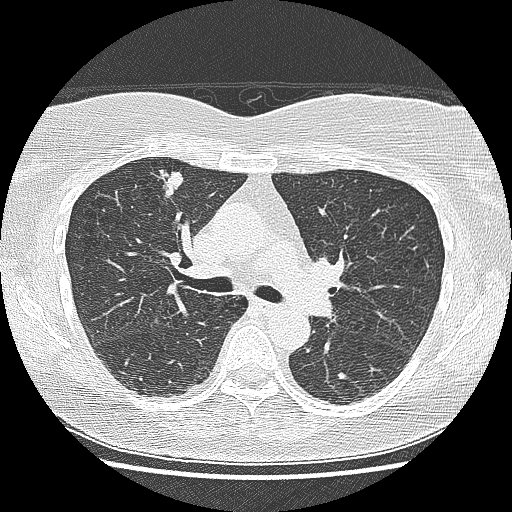
Low-dose screening chest CT, one axial slice. Position 94 of 155 along the scan axis. Reconstruction kernel LUNG. Lung window (W 1500 / L -600 HU). 512 × 512 image matrix, field of view 330 × 330 mm.
Structures marked on this image (expert manual segmentation):
- lesion 1 (tumor, upper lobe of right lung): bounding box <158,167,185,198> (left, top, right, bottom; pixels)